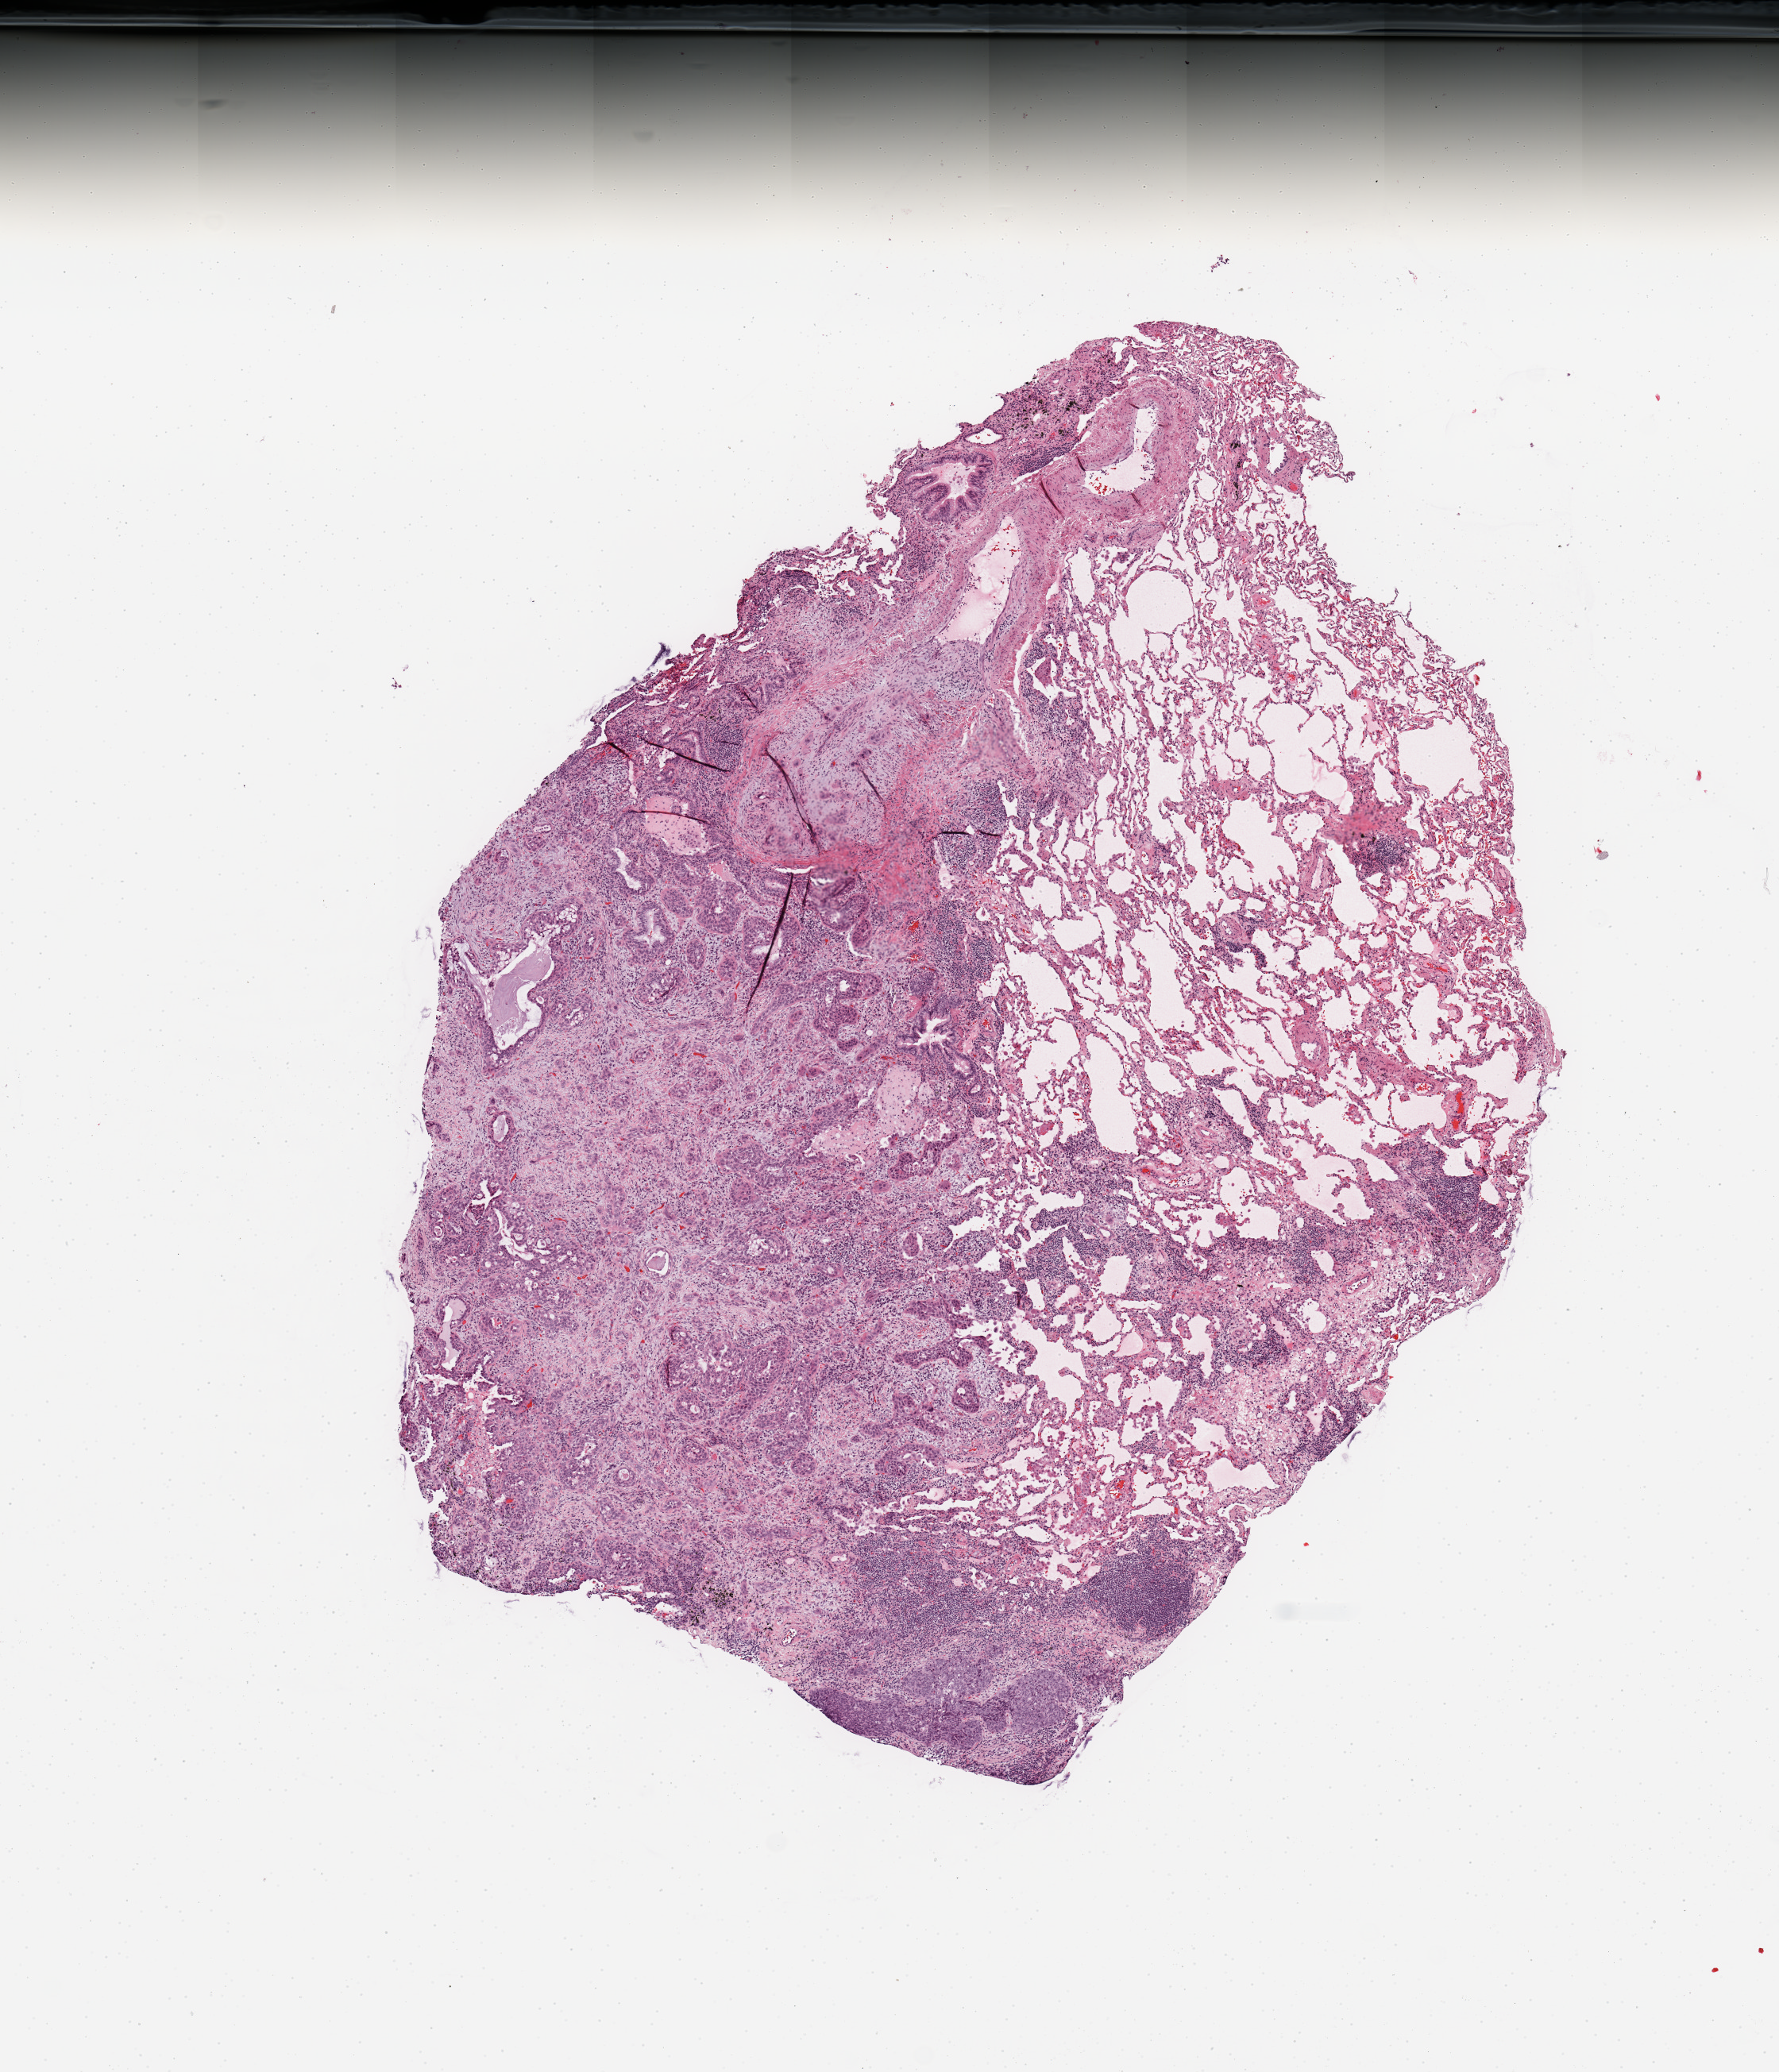
Digitized H&E-stained tissue section (whole slide) — a low-resolution overview of the entire scanned area, about 8.9 x 10.3 mm. Tumour tissue sample, sampled site: lung. Patient: male, age 68 years. Histologic grade: G3 (poorly differentiated). Slide review estimates, as recorded: tumour nuclei 55%, necrosis 3%.
Diagnosis: Squamous cell carcinoma, NOS. AJCC pathologic stage: IB. Primary tumour site (as recorded): left lower lobe.